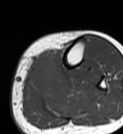
MRI of an extremity soft-tissue mass, one axial slice; position 19 of 68 along the scan axis; MR volume resampled by the dataset authors to the PET/CT grid (not the native acquisition matrix); 123 × 134 image matrix. Female patient. From the clinical record (not read from this slice): histological type: extraskeletal high grade osteogenic sarcoma; grade: high; site of the primary tumour: left calf.
Outlined on this slice (expert contour drawn on MRI and transferred to this co-registered scan by the dataset authors):
- gross tumour volume (mass): bounding box [x1, y1, x2, y2] px = [28, 55, 57, 94]